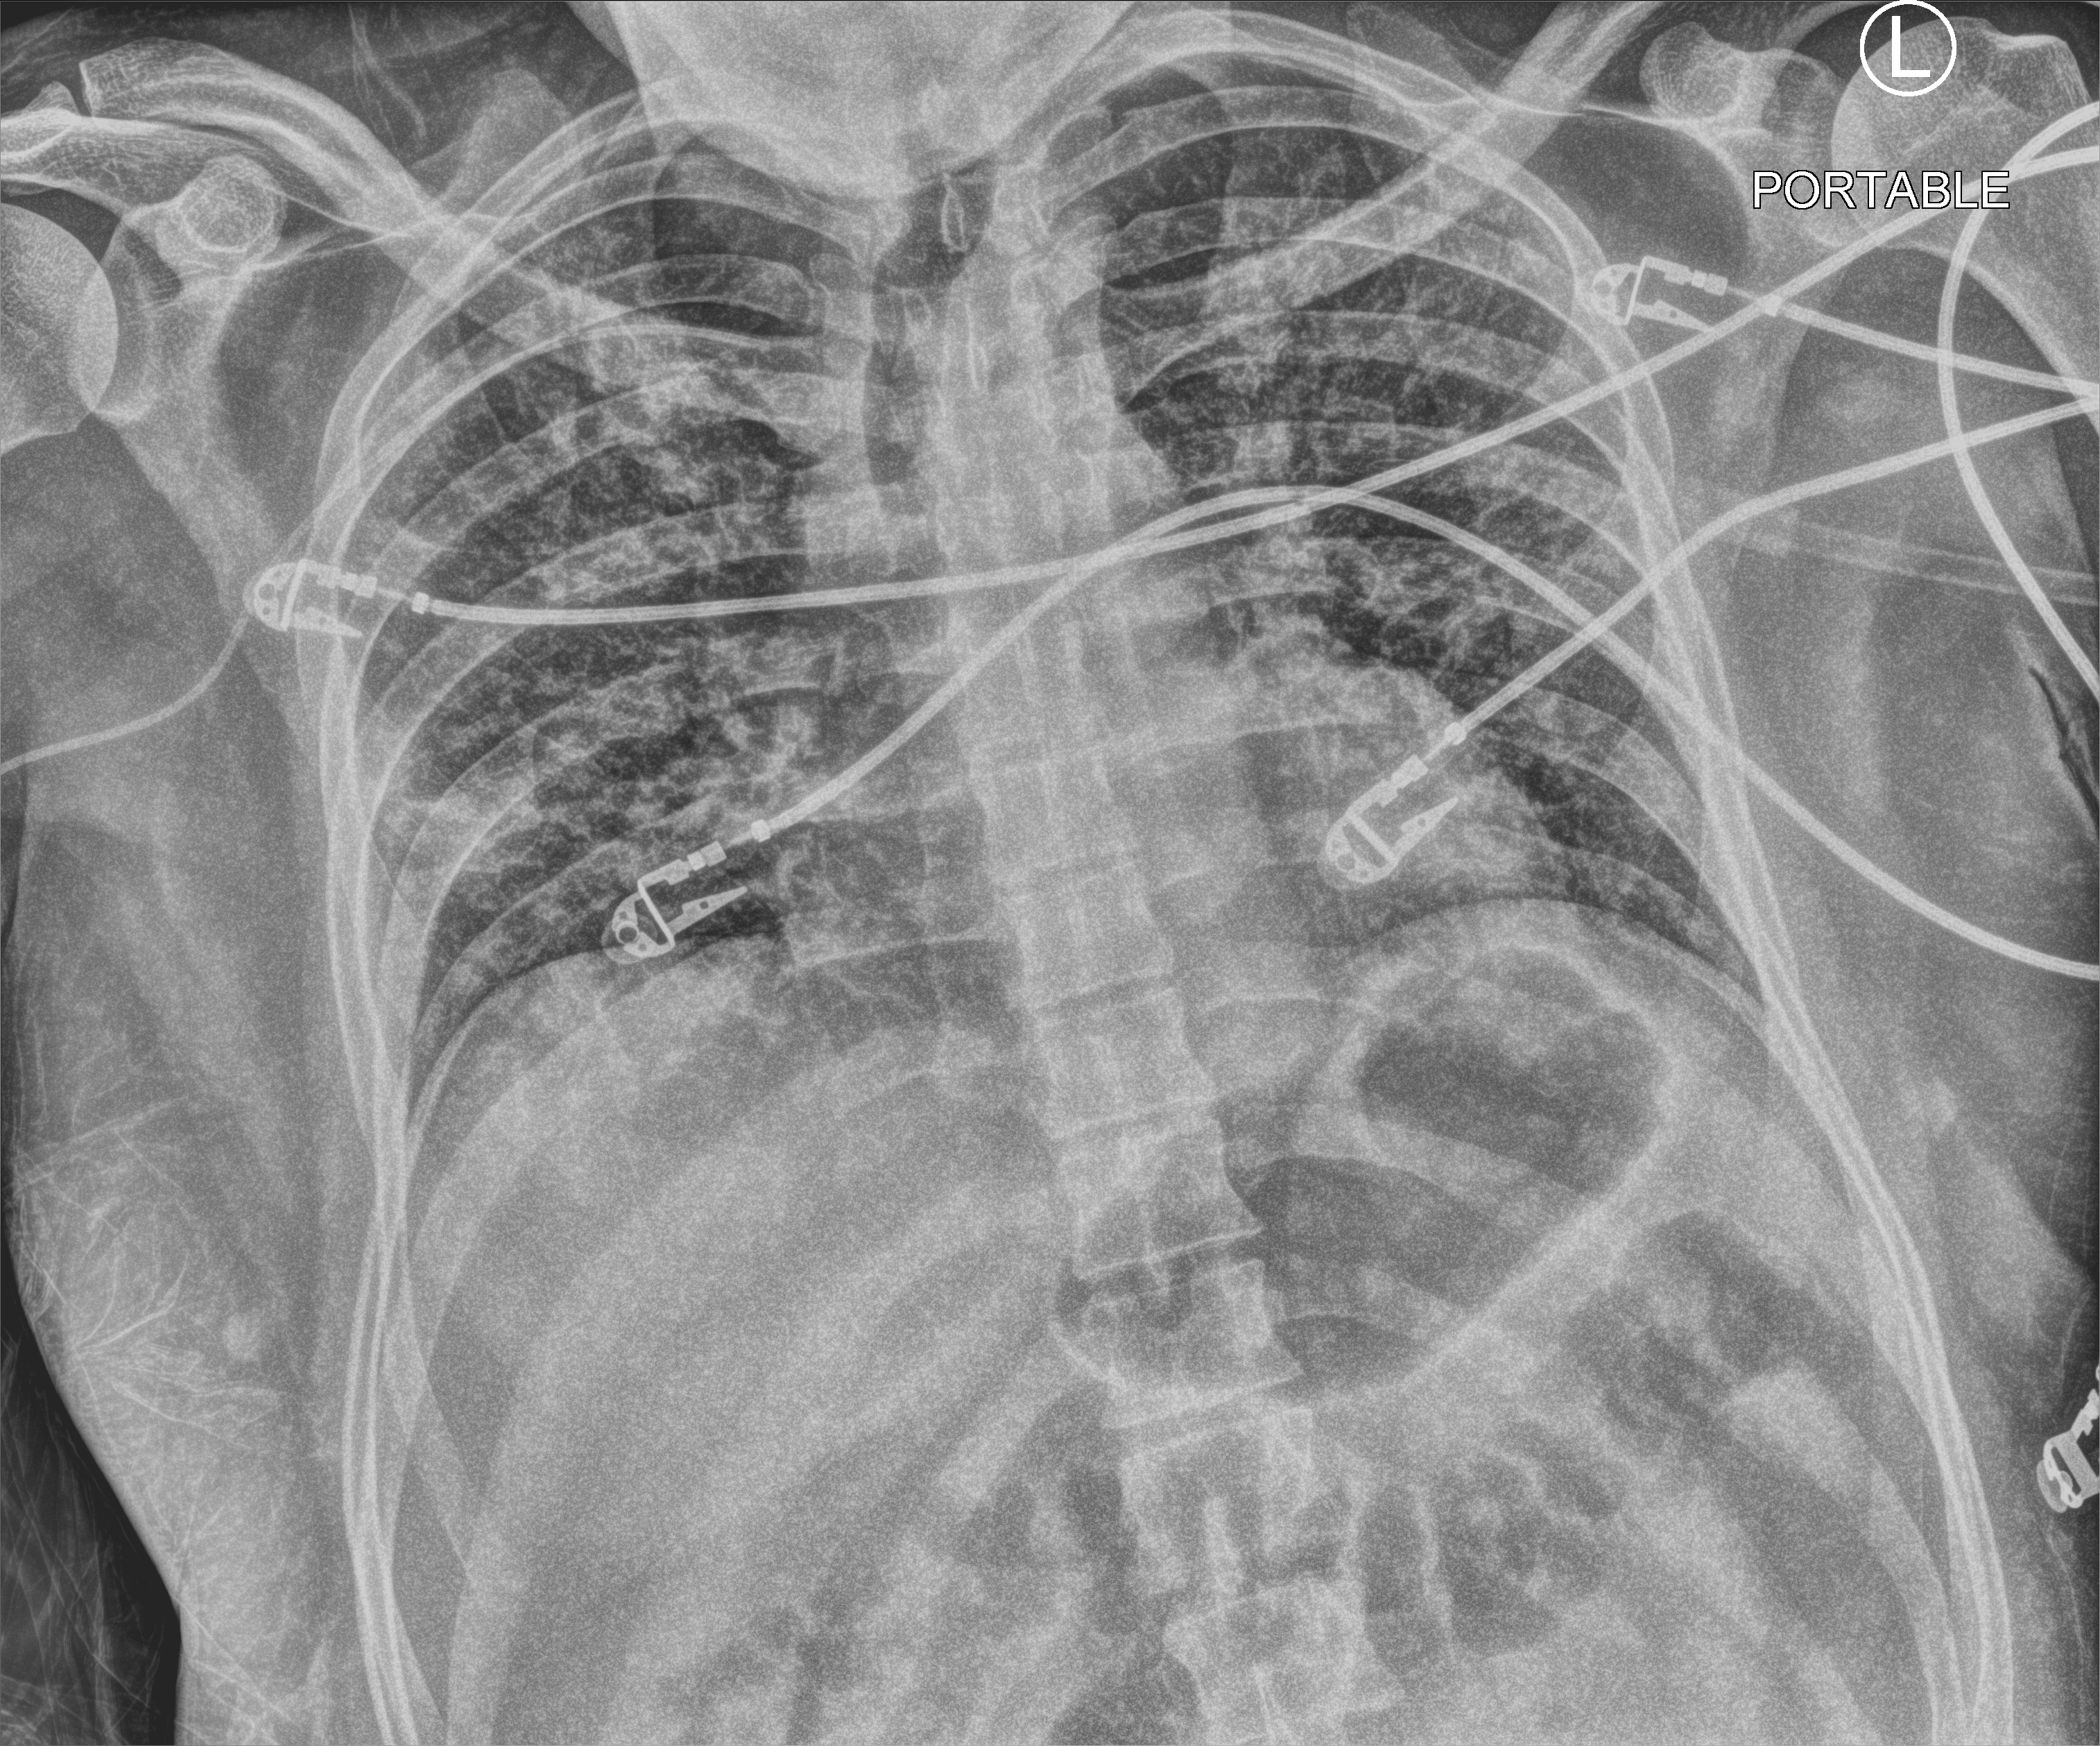
Bedside chest radiograph (computed radiography), anteroposterior (AP) projection. Male patient hospitalised with COVID-19, age 18–59 years.
From the hospital-stay record, not from the radiograph (when in the stay this image was taken is not recorded): admitted to intensive care during this hospital stay: yes; mechanically ventilated during this hospital stay: yes; diabetes (admission record): no.